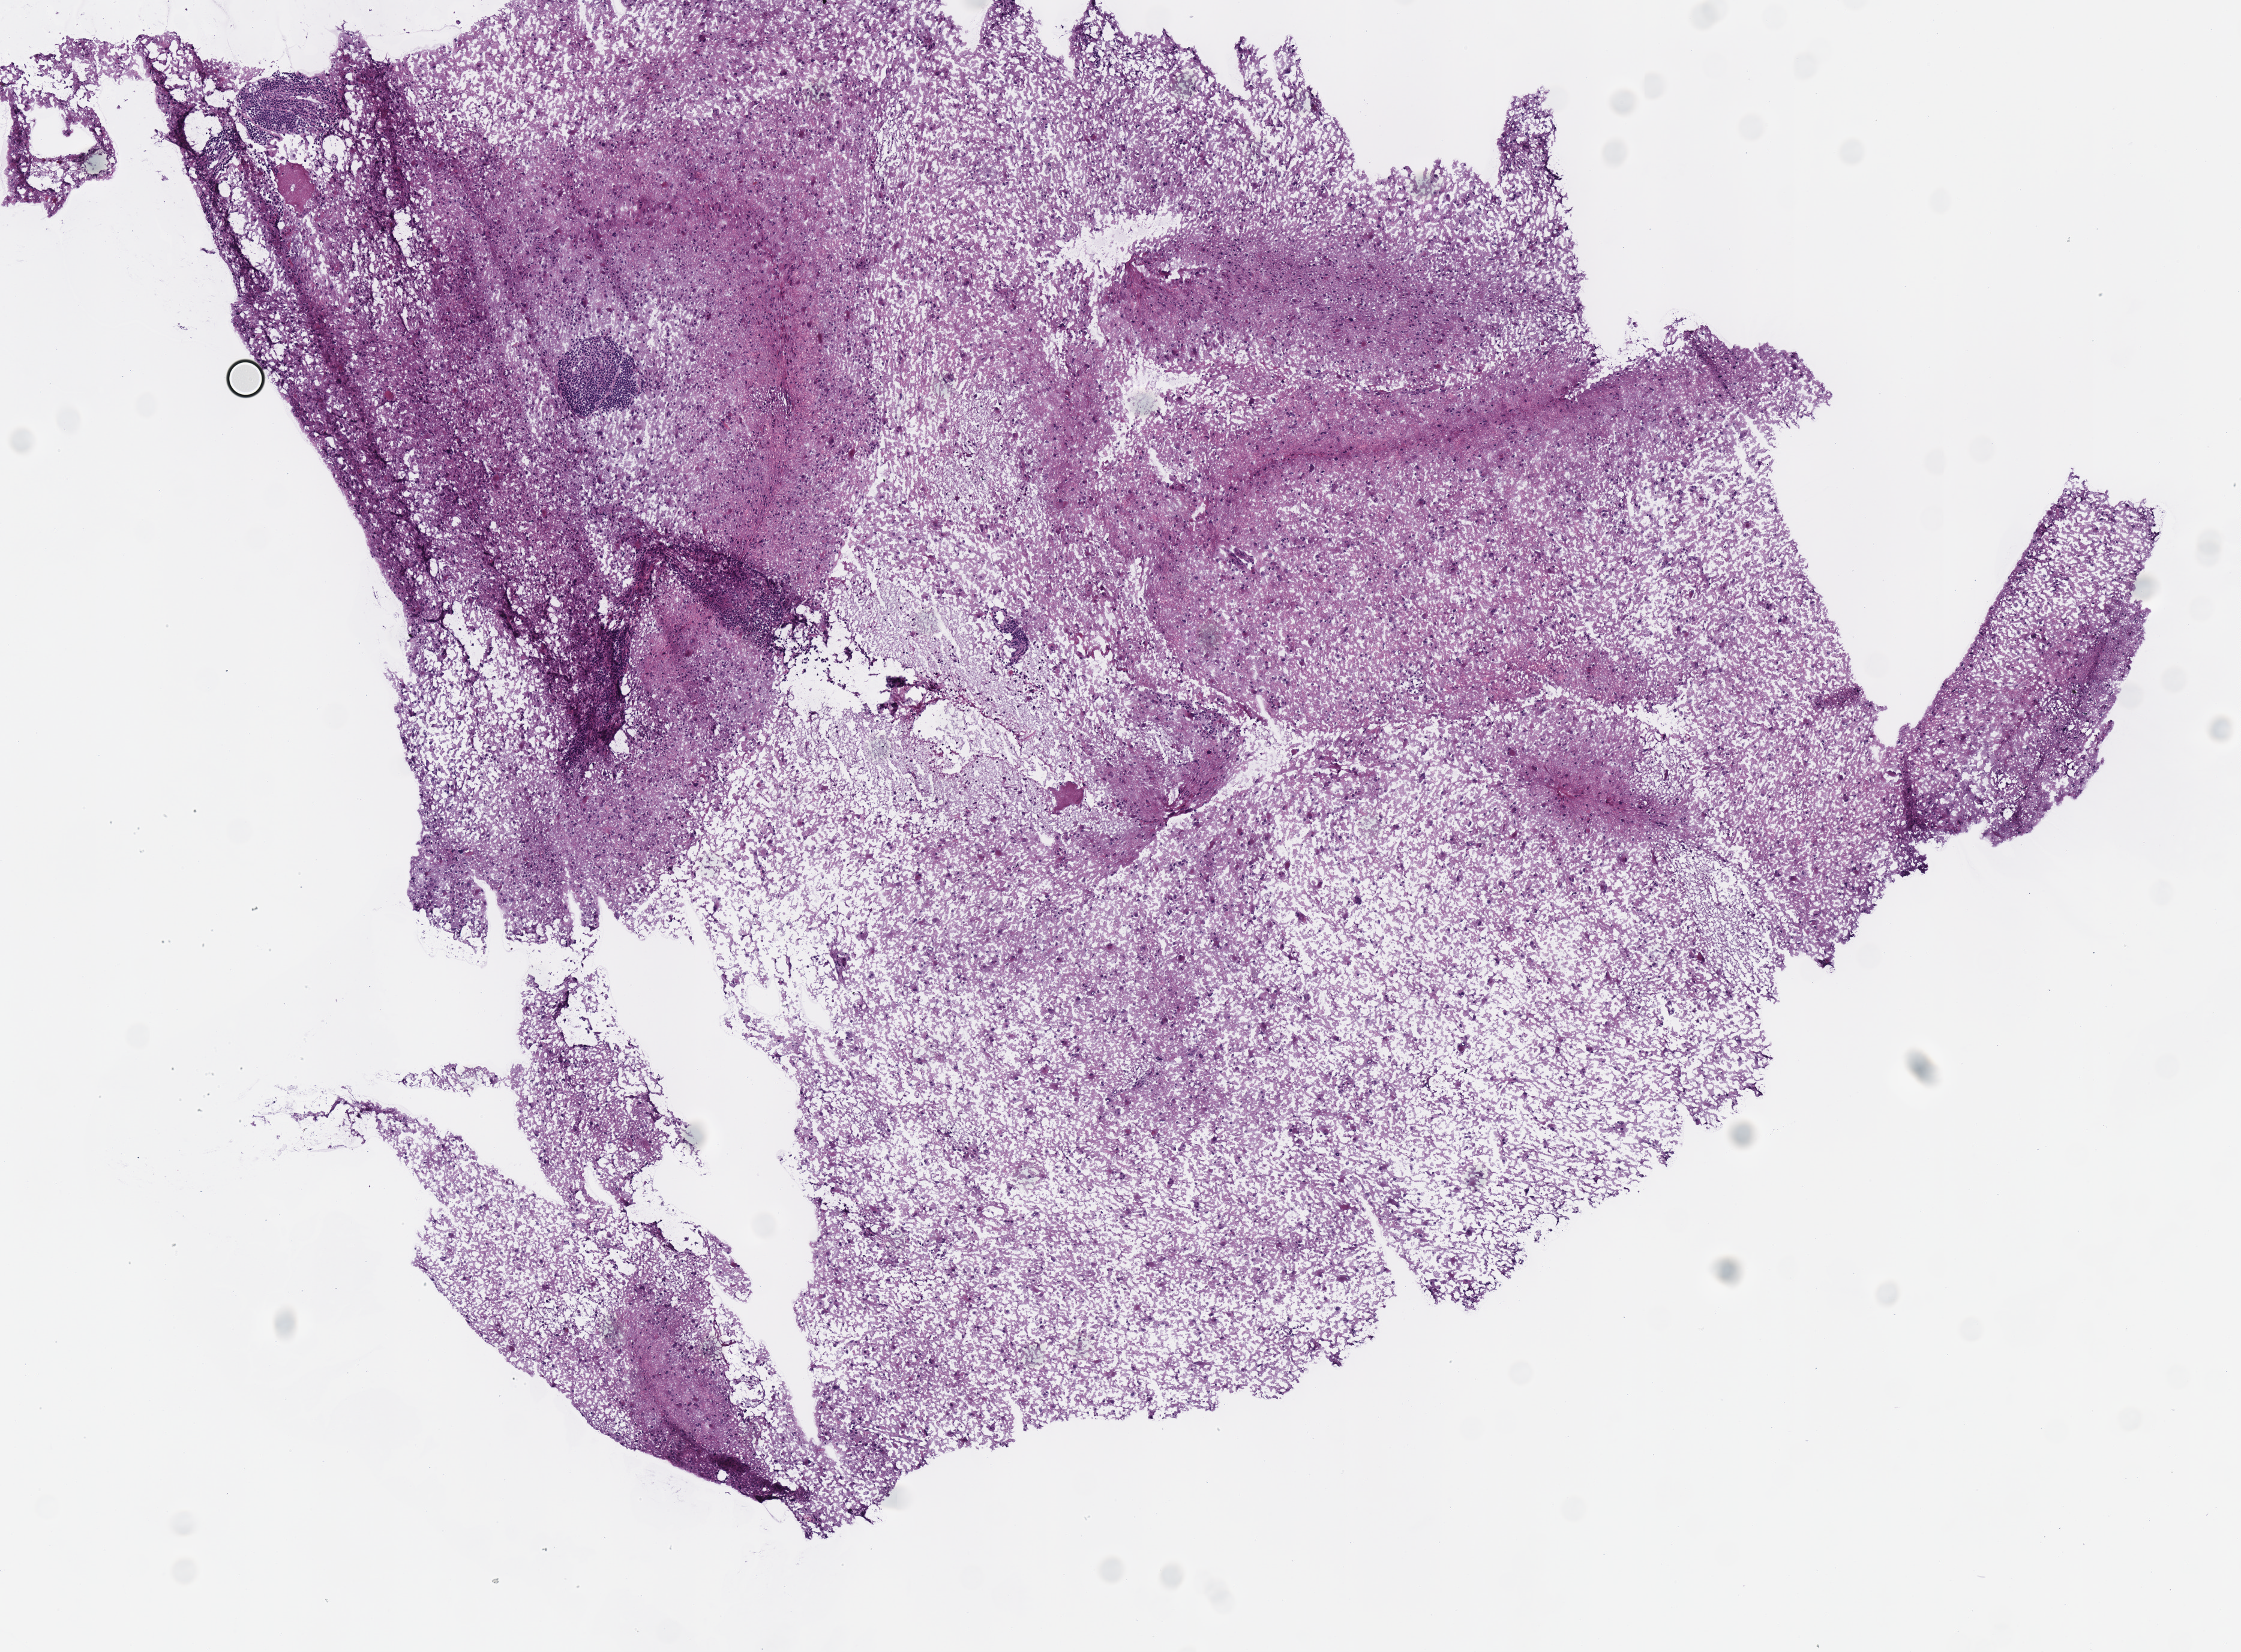
Digitized H&E-stained tissue section (whole slide), a low-resolution overview of the entire scanned area, about 7.3 x 5.4 mm (acquisition: 40x scan); frozen section from the top of the tissue portion; sample: primary tumour, brain. Male patient; age at initial diagnosis 53 years. Histologic grade: G3 (poorly differentiated). Slide review estimates, as recorded: tumour cells 100%, tumour nuclei 60%, normal cells 0%, stromal cells 0%, necrosis 0%.
Diagnosis: Astrocytoma, anaplastic (cerebrum).